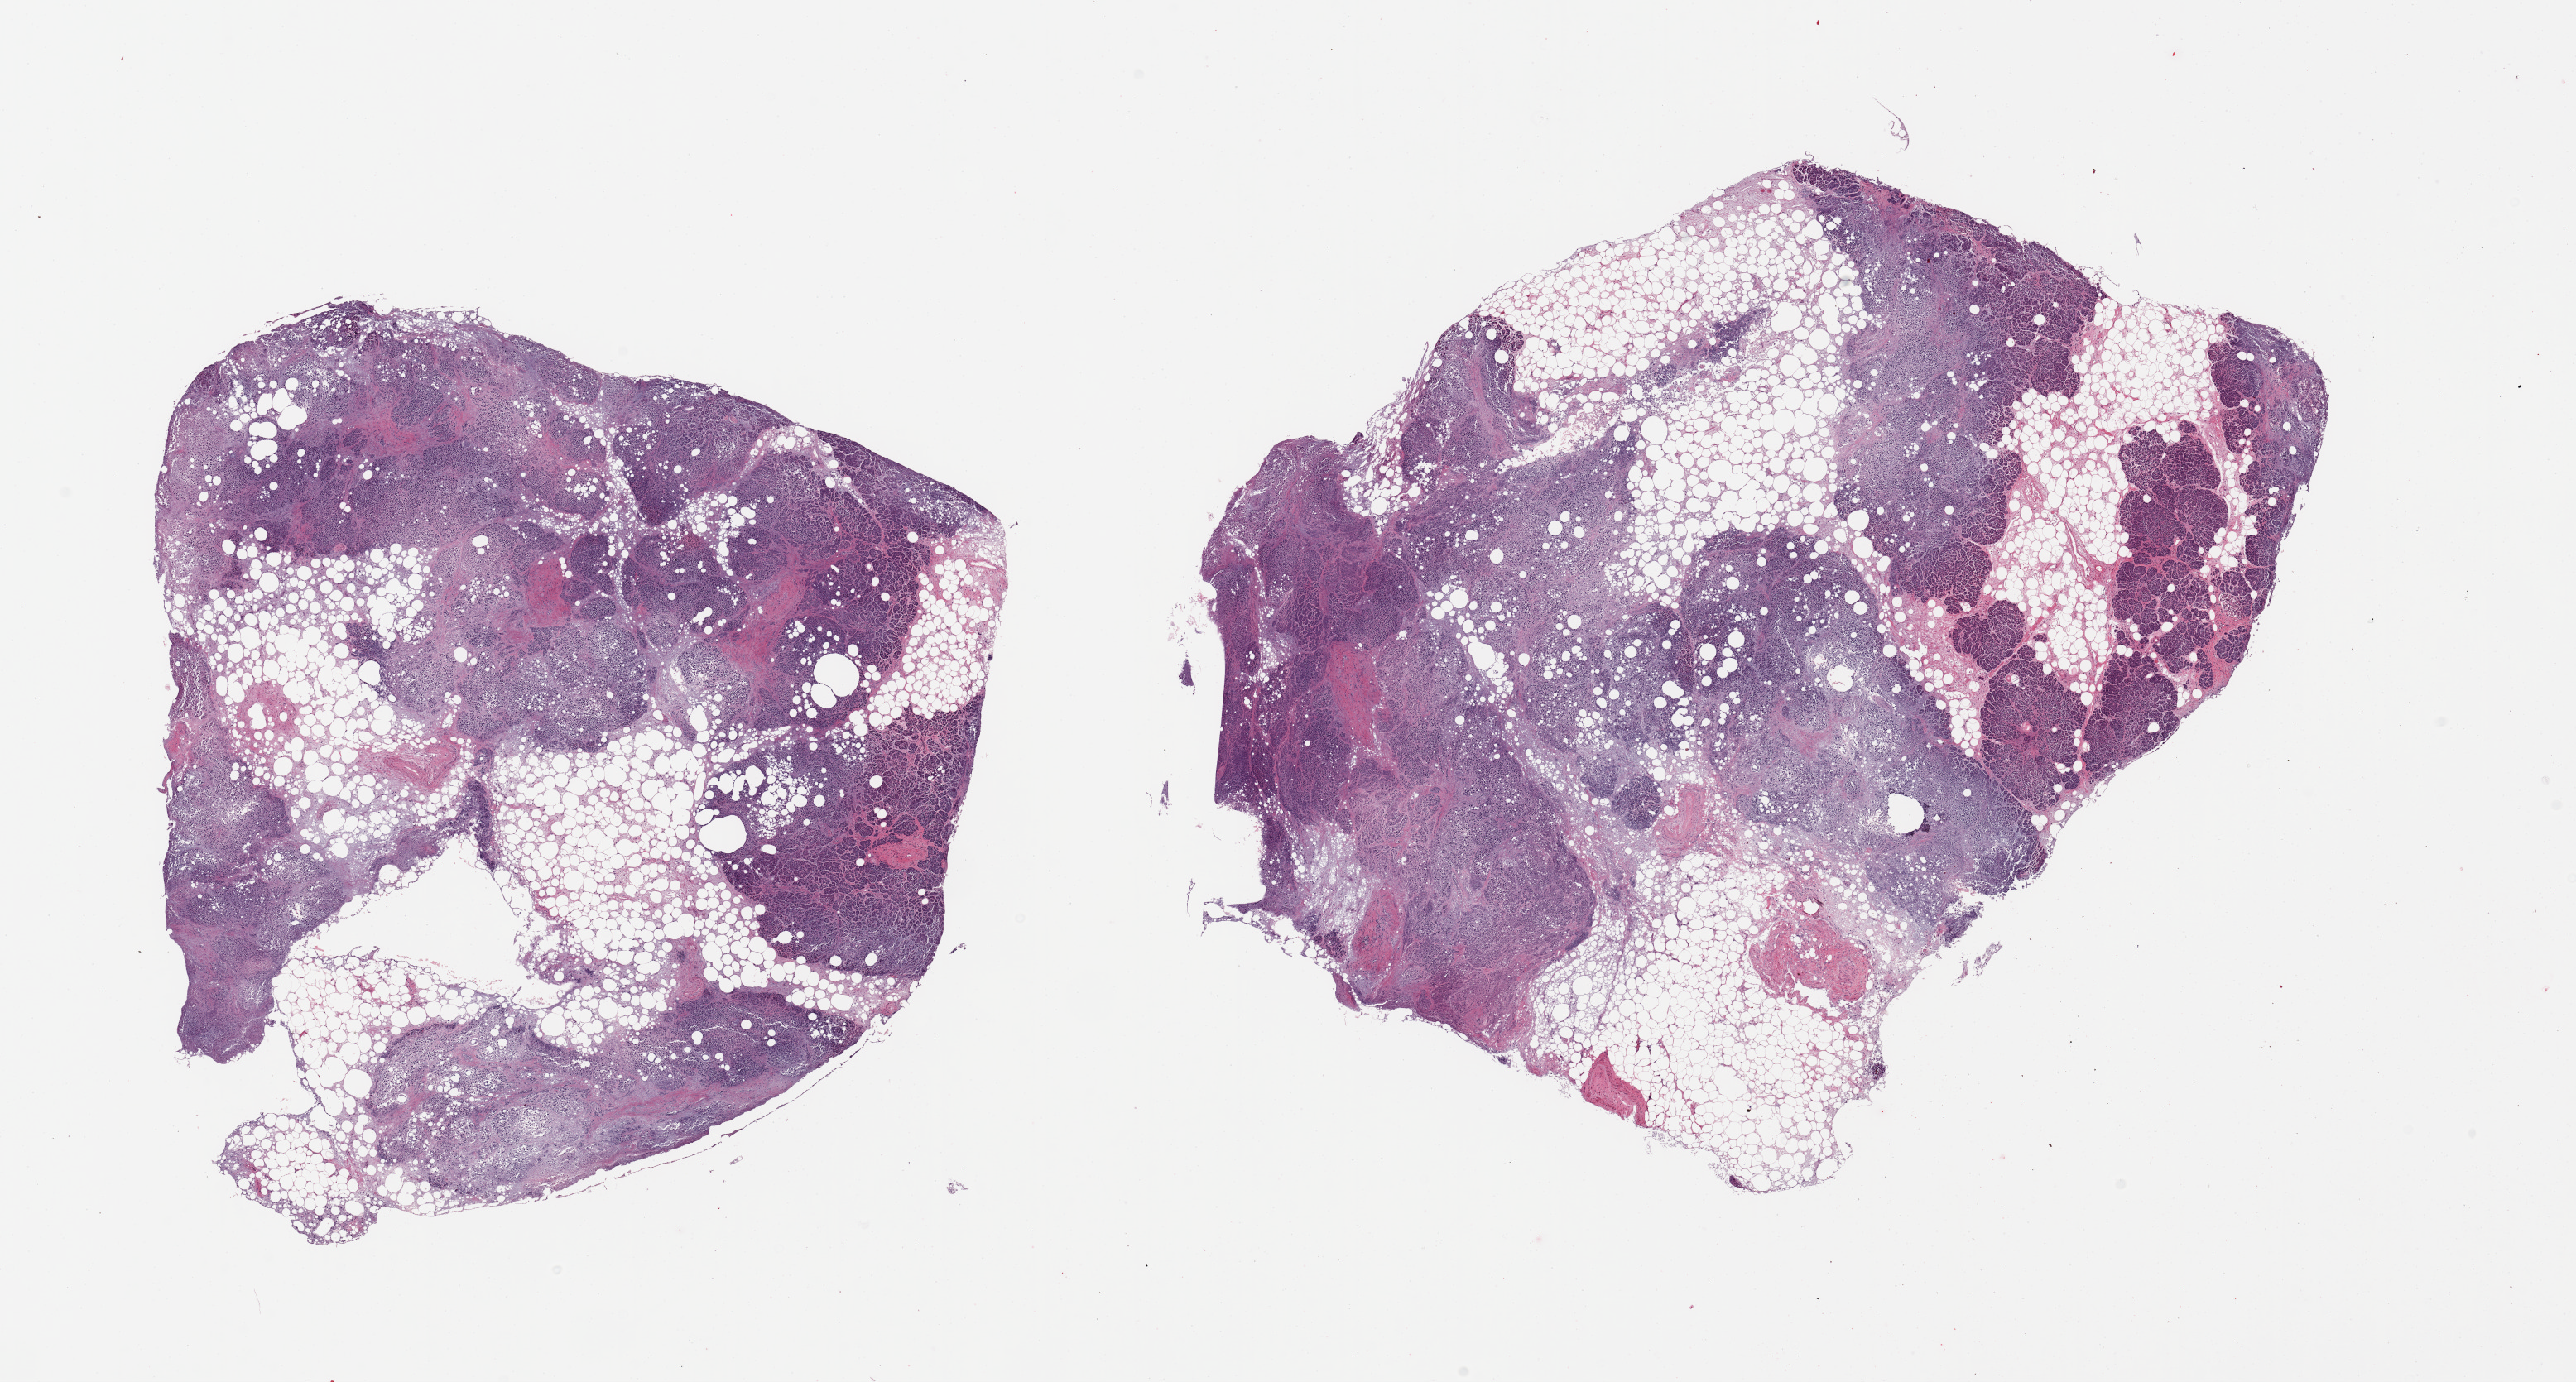
Whole-slide image, H&E stain, brightfield, a low-resolution overview of the entire scanned area, about 24.6 x 13.2 mm (acquisition: 20x scan), PAXgene-fixed paraffin-embedded (PFPE) section, sampled site (target tissue): pancreas, tissue donor sample. Male donor.
Reviewer comment on this tissue sample: 2 pieces; largely autolyzed 50%; internal fat.